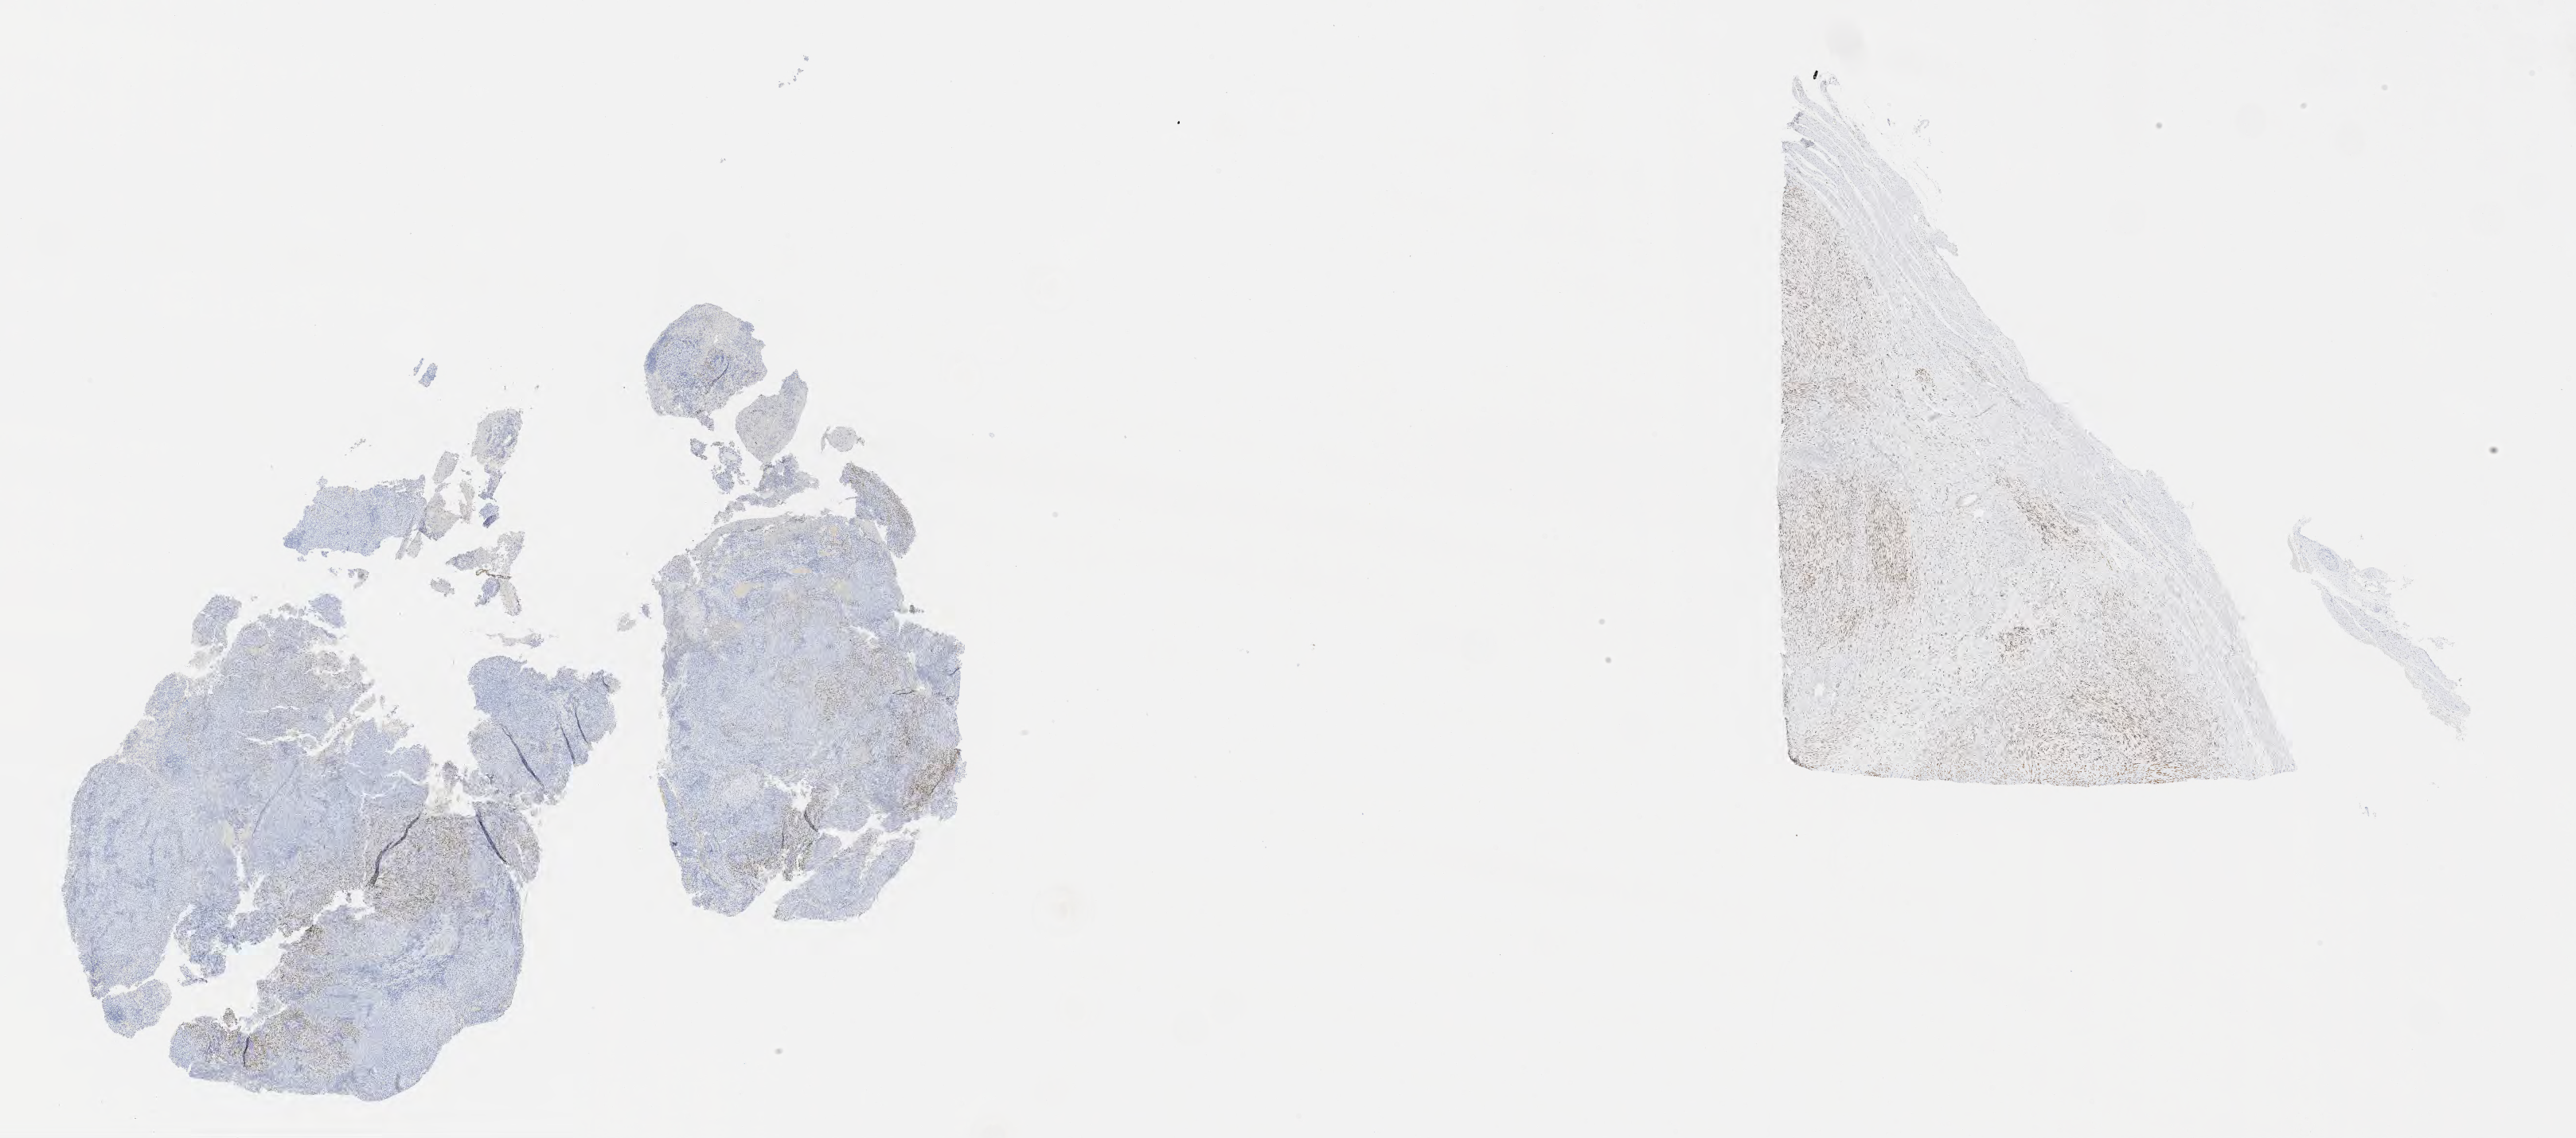
Immunohistochemistry (IHC) whole-slide image stained for estrogen receptor (ER) — a low-resolution overview of the entire scanned area, about 26.2 x 11.6 mm, specimen: tumor tissue, anatomic site: cervix. Patient female; aged 70.
* histologic diagnosis: Squamous cell carcinoma, large cell, nonkeratinizing, NOS